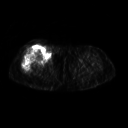
FDG PET of an extremity soft-tissue mass (from a PET/CT study), one axial slice. Position 252 of 311 along the scan axis. 3.27 mm slice thickness. 128 × 128 image matrix. Patient: female, 57 years. Case-level facts recorded for this patient, not image findings: histological type: pleiomorphic undifferentiated sarcoma; grade: high; site of the primary tumour: right quadricep.
Outlined on this slice (expert contour drawn on MRI and transferred to this co-registered scan by the dataset authors):
- tumour plus oedema (research contour): bounding box [x1, y1, x2, y2] px = [23, 45, 50, 72]
- tumour (research contour): [23, 45, 50, 72]